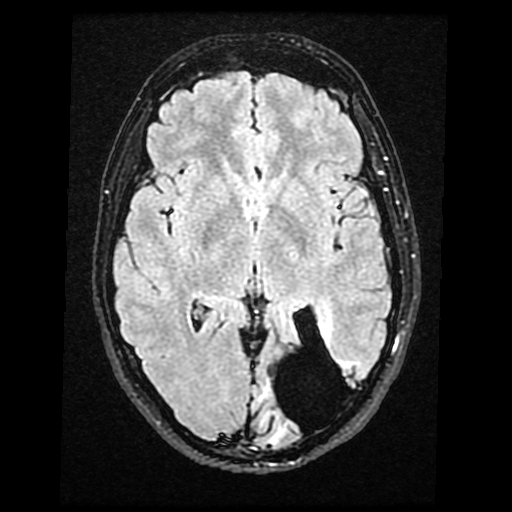
Brain MRI from a brain-tumour surgery series, one axial slice; slice 22 of 40 in the series (ordered by position); T2 FLAIR; 4 mm slice thickness; 512 × 512 image matrix, field of view 240 × 240 mm. Case-level facts recorded for this patient, not image findings: histopathology: Glioma with ependymal features; WHO grade: 2; tumour location: Left Parietal.
Structures marked on this image (manually delineated by an expert):
- tumour: bounding box (x1, y1, x2, y2) in pixels: (276, 414, 296, 438)